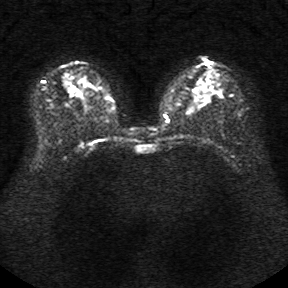
Breast MRI, one axial slice; diffusion-weighted series; image 2 of 4 stored at this slice position (different b-values; order by instance number); 1.5 T; 5 mm slice thickness; 288 × 288 image matrix, field of view 340 × 340 mm. Female patient.
Structures marked on this image (outlined manually by an expert reader):
- tumour on diffusion-weighted imaging: box from (x=200, y=94) to (x=209, y=101) px